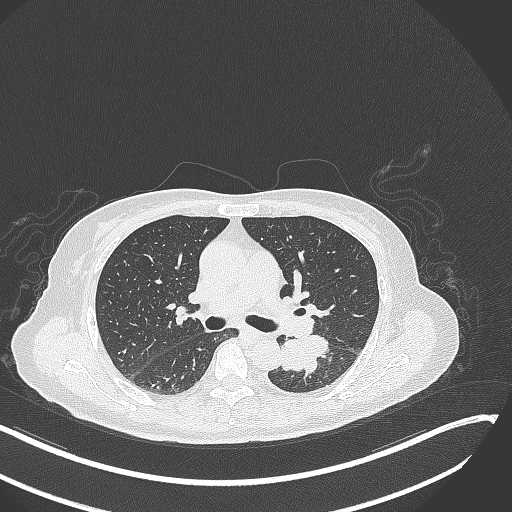
Chest CT, one axial slice. Slice 170 of 342 in the series (ordered by position). Reconstruction kernel B70f. Lung window (W 1500 / L -600 HU). 512 × 512 image matrix, field of view 400 × 400 mm. Female patient, age 64 years. Case-level facts recorded for this patient, not image findings: clinical TNM (as recorded): T3 N1 M1; histopathological grade: G3.
Annotated regions visible in this slice (bounding box drawn by a radiologist):
- lung tumour (recorded histology: small cell carcinoma): bounding box <280,333,330,376> (left, top, right, bottom; pixels)